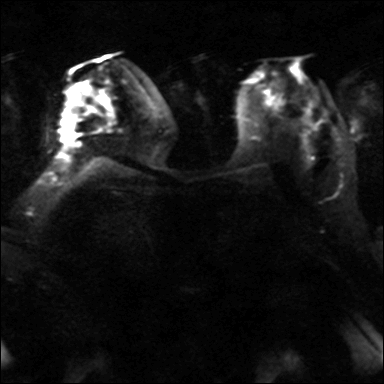
Breast MRI, one axial slice. Diffusion-weighted series; image 2 of 4 stored at this slice position (different b-values; order by instance number). 3 T. 4 mm slice thickness. 384 × 384 image matrix, field of view 320 × 320 mm. Female patient.
Annotated regions visible in this slice (manually delineated by an expert):
- tumour on diffusion-weighted imaging: bounding box [x1, y1, x2, y2] px = [63, 128, 75, 143]